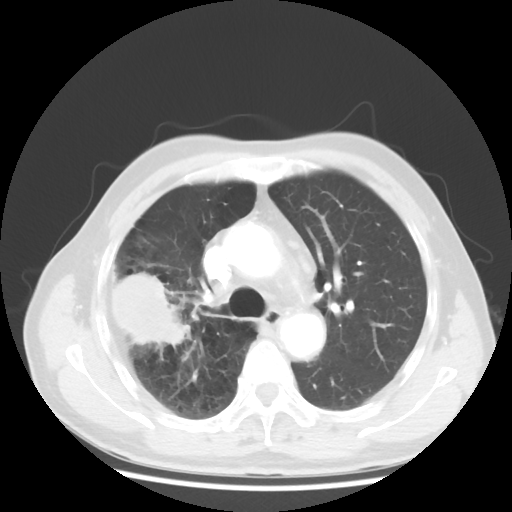
Chest CT, one axial slice. Slice 33 of 50 in the series (ordered by position). 120 kVp. Lung window (W 1500 / L -600 HU). 512 × 512 image matrix, field of view 360 × 360 mm. Male patient, age 69 years. From the clinical record (not read from this slice): clinical TNM (as recorded): T3 N0 M0; histopathological grade: G3.
Outlined on this slice (bounding box drawn by a radiologist):
- lung tumour (recorded histology: adenocarcinoma): bounding box [x1, y1, x2, y2] px = [106, 268, 192, 349]